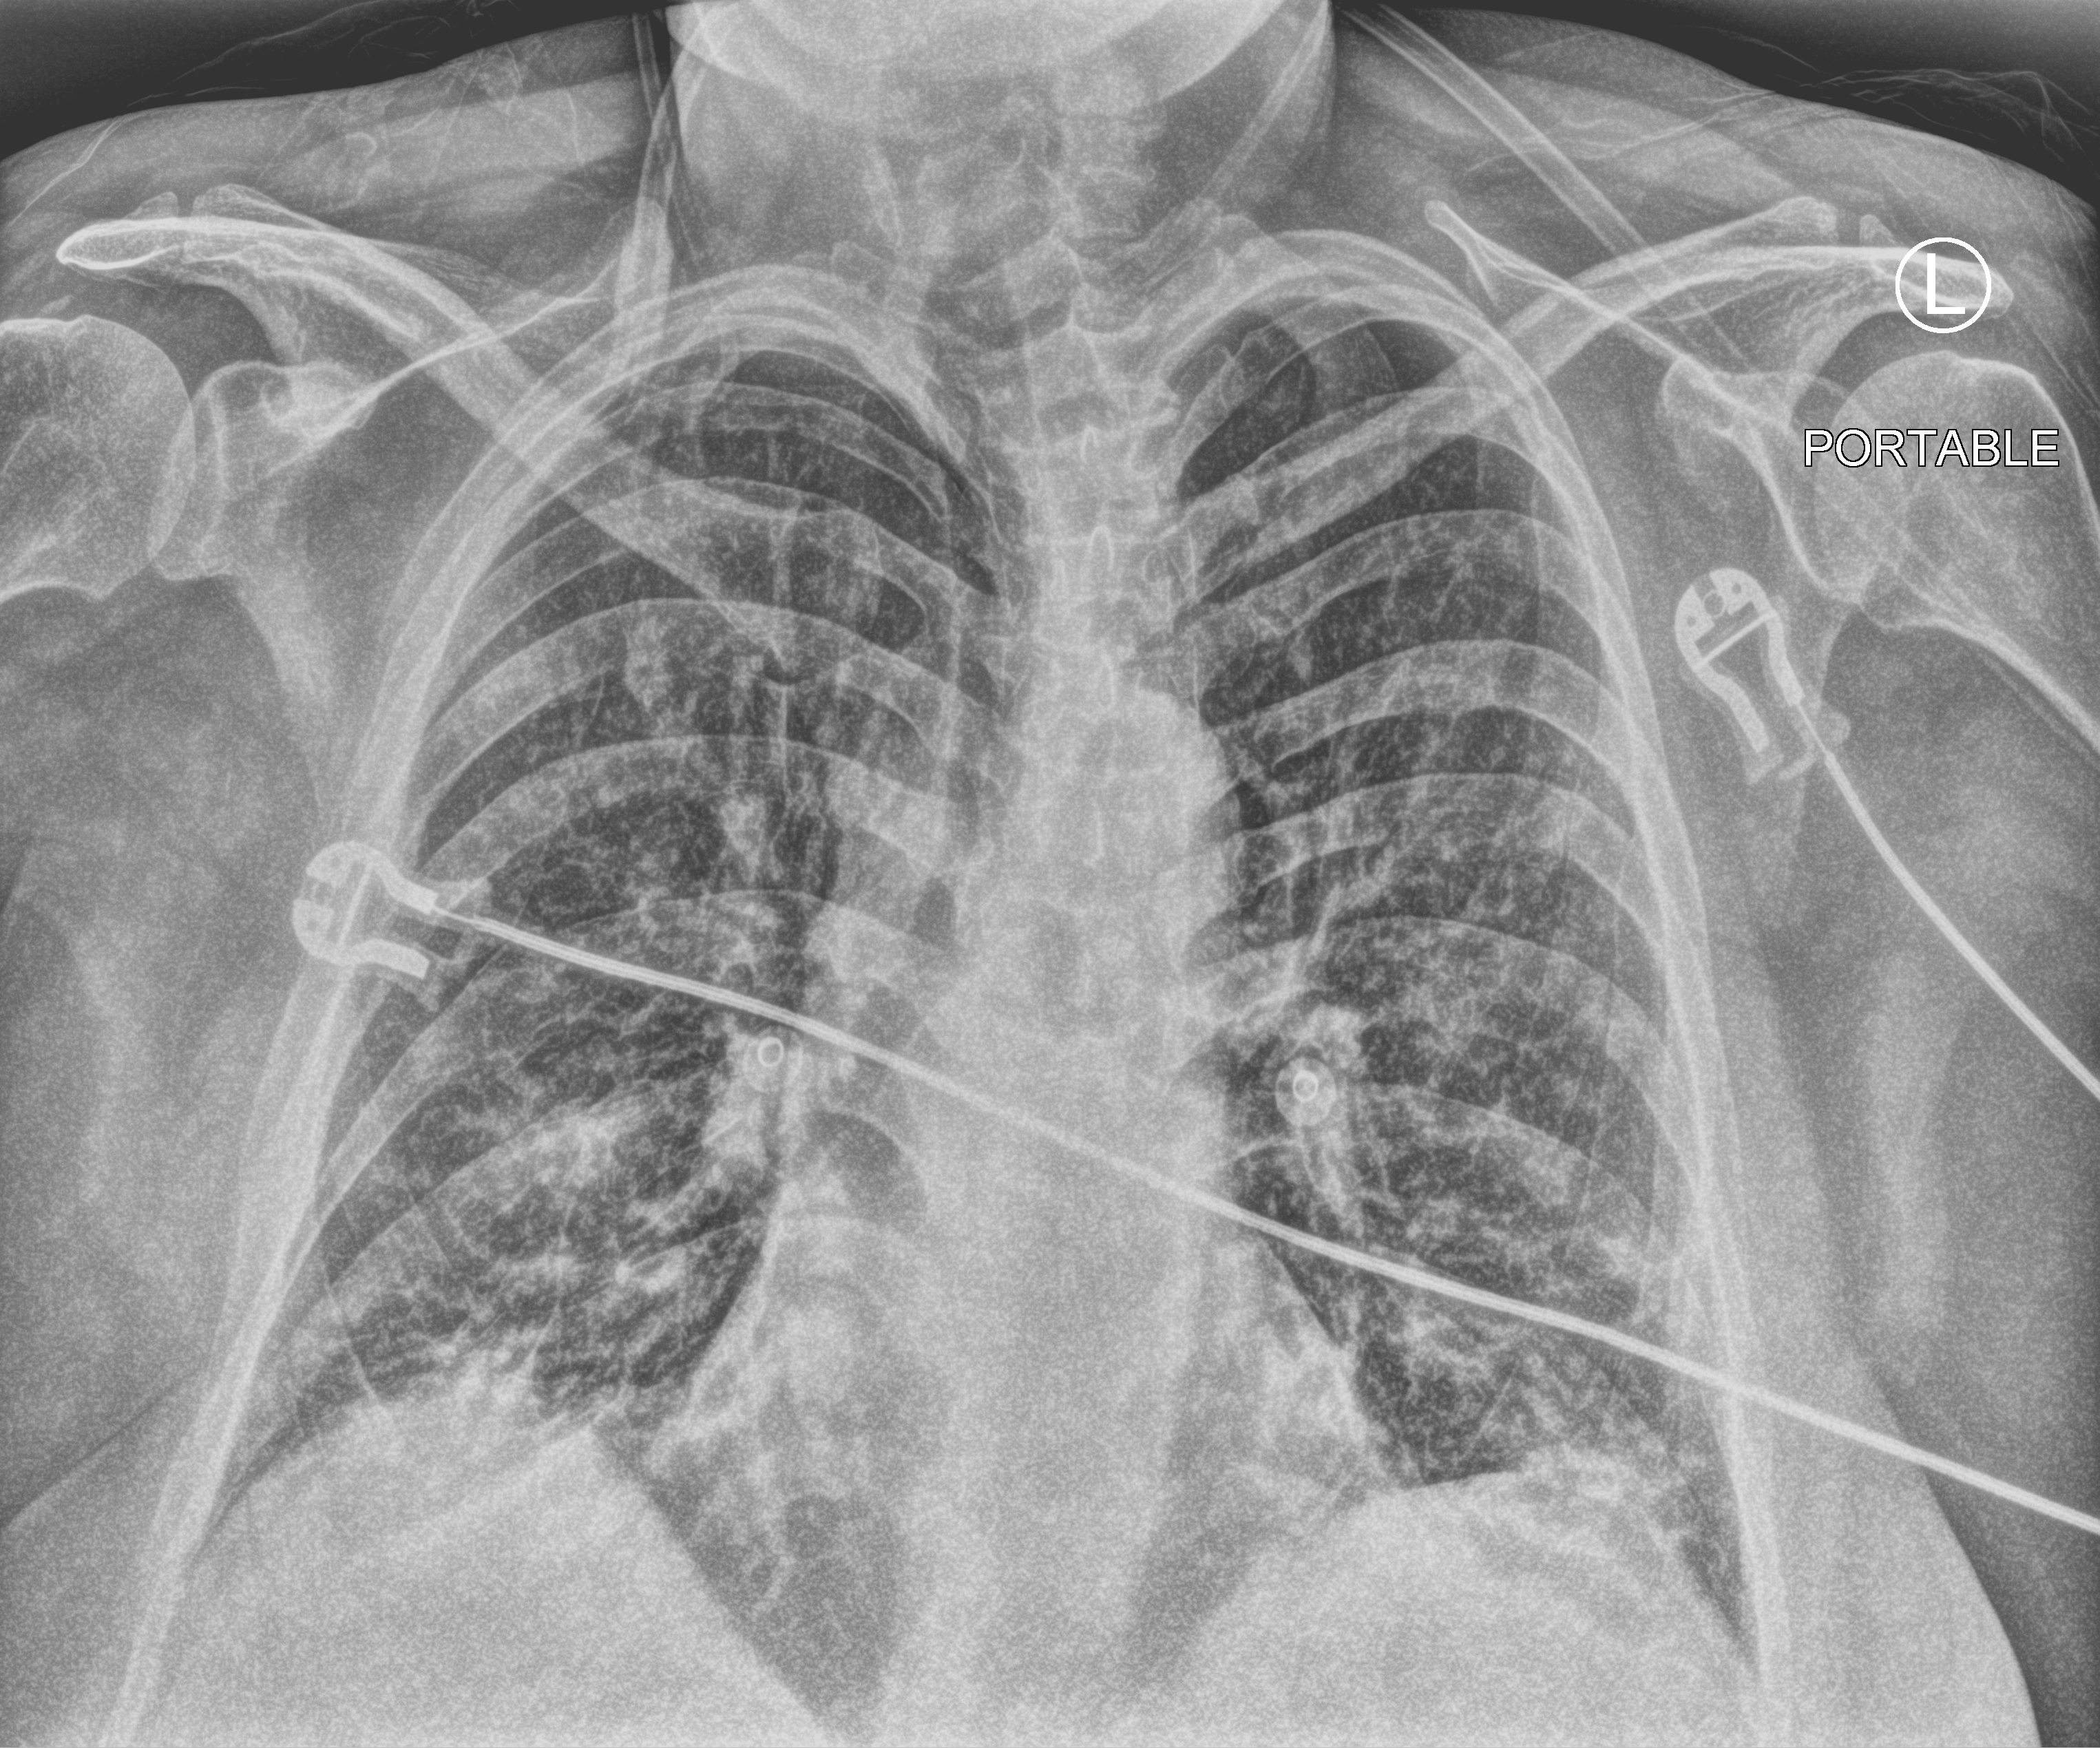
Chest X-ray (portable), anteroposterior (AP) projection. Patient hospitalised with COVID-19; female, aged 18–59 years.
From the hospital-stay record, not from the radiograph (when in the stay this image was taken is not recorded): other chronic lung disease (admission record): yes; mechanically ventilated during this hospital stay: no.